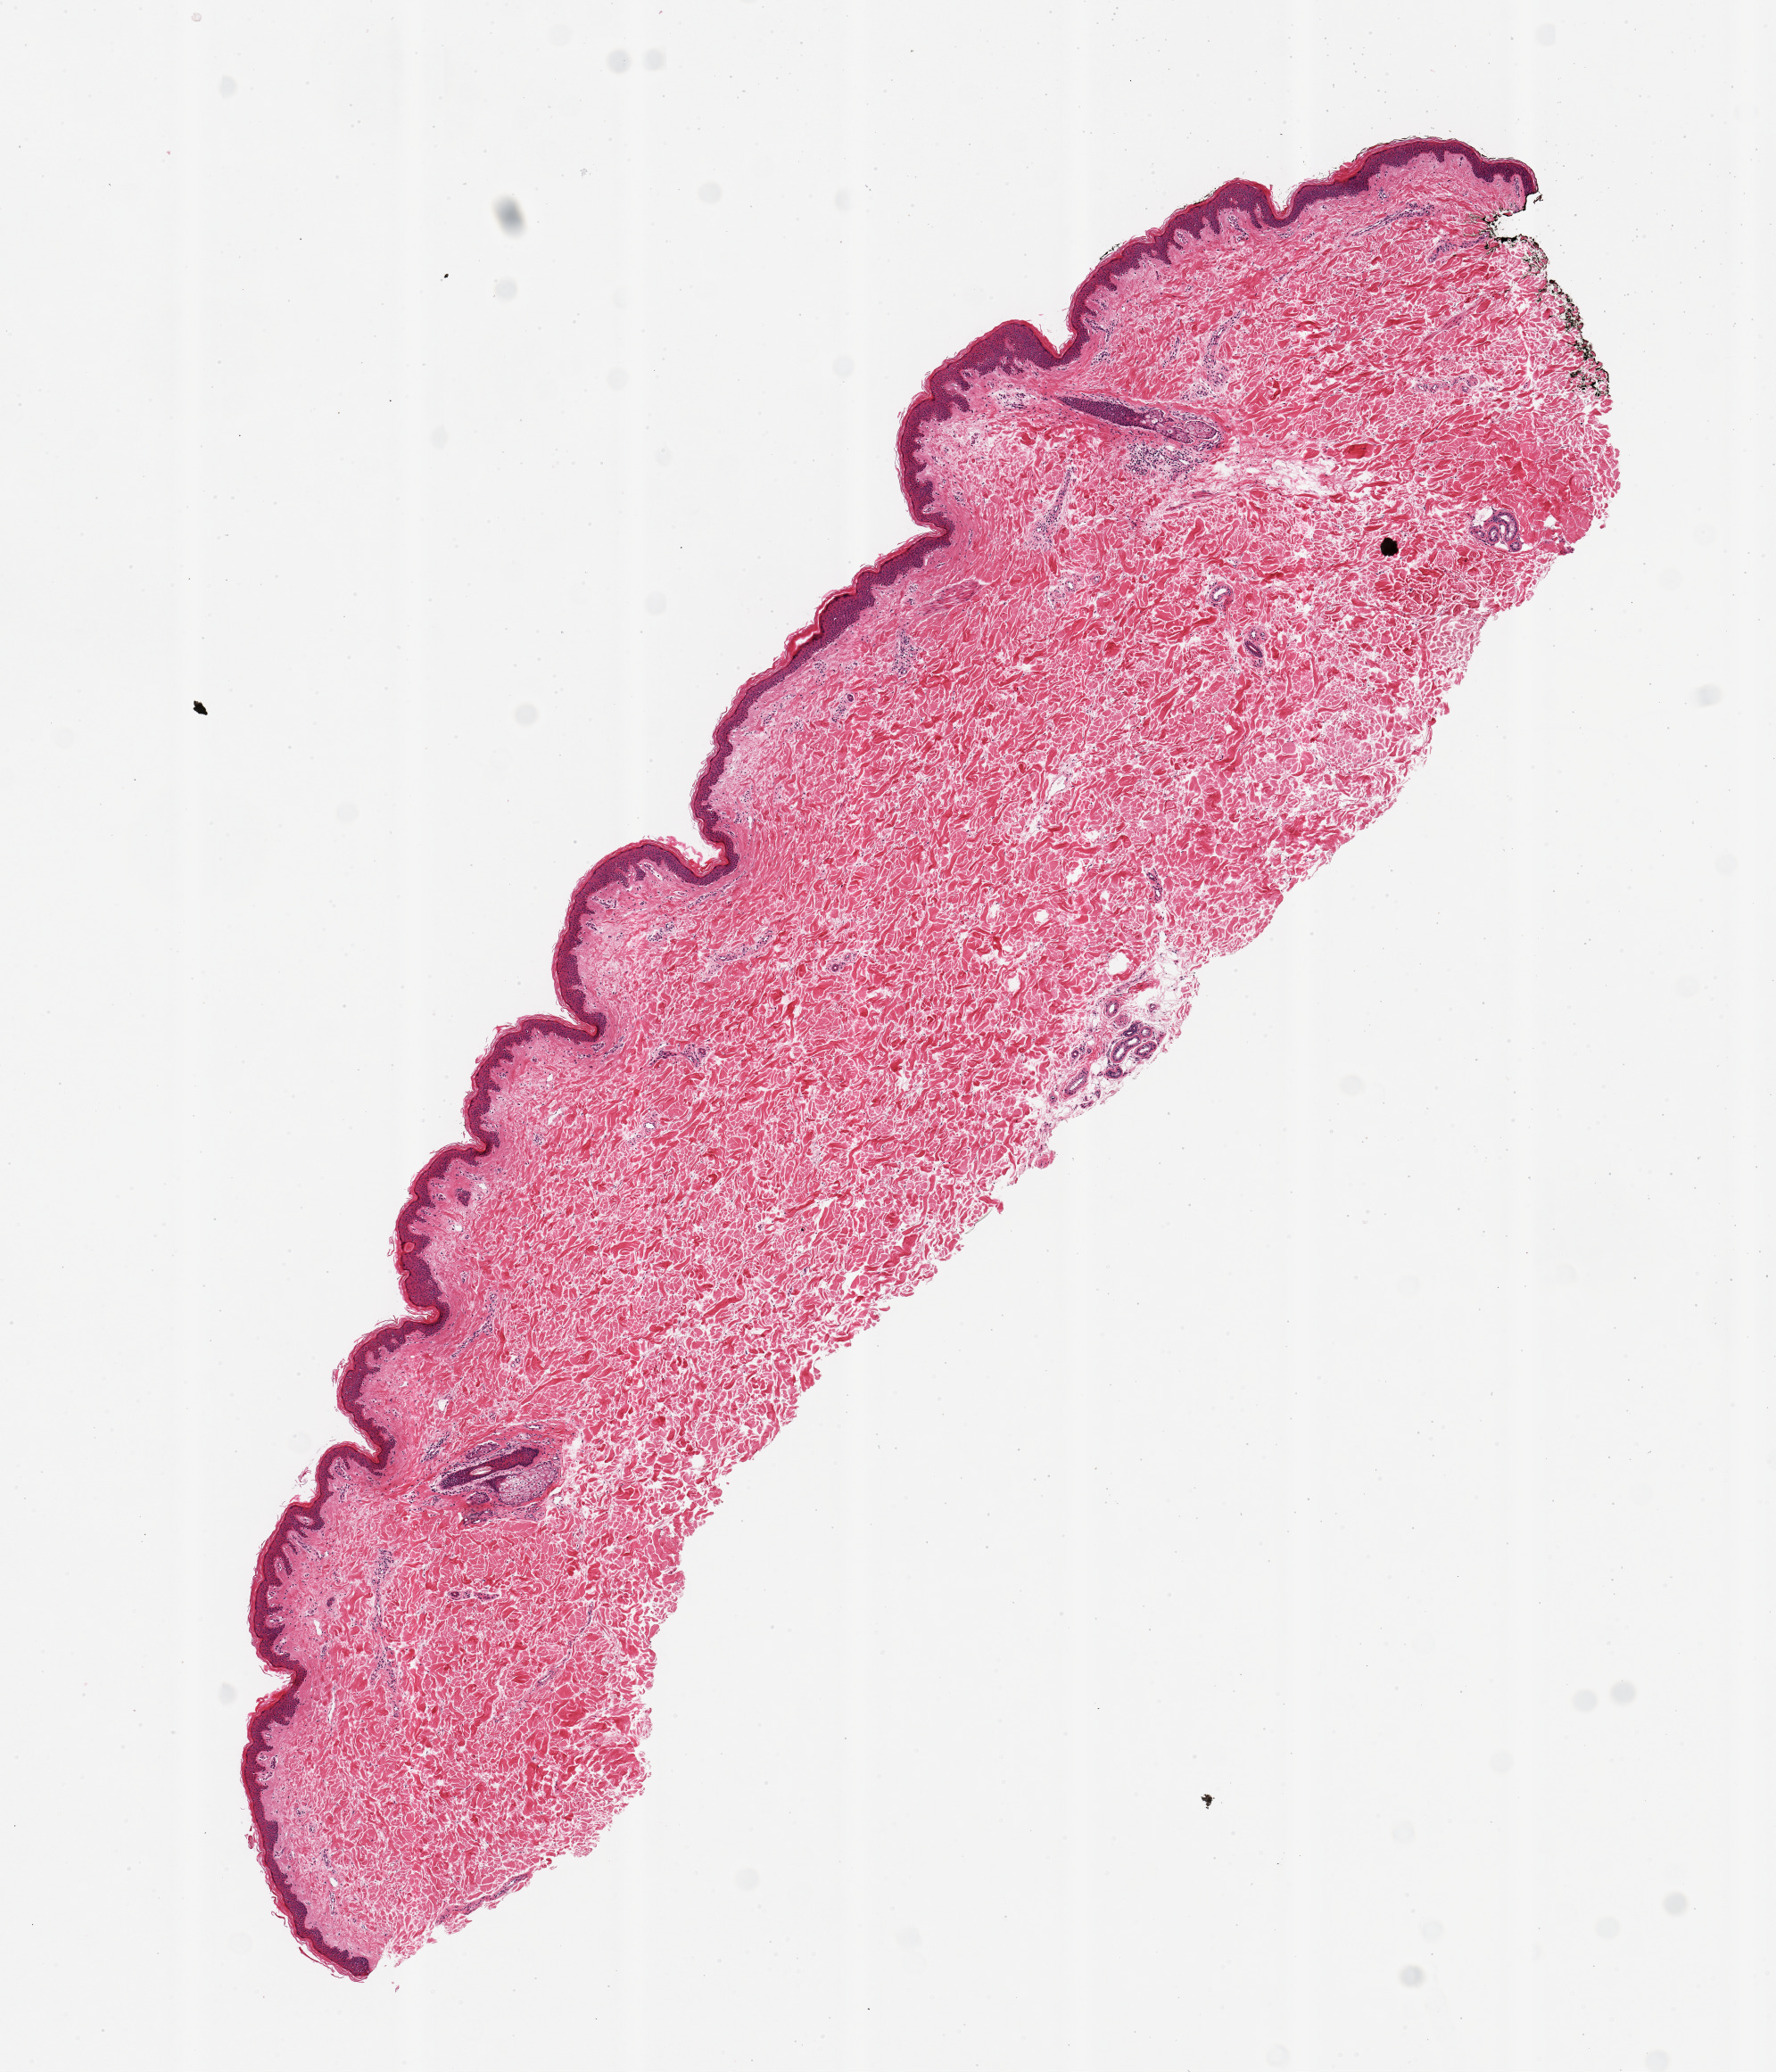
Whole-slide image, haematoxylin and eosin stain, shown as a low-resolution overview of the whole scanned area (about 7.9 x 9.2 mm), PAXgene-fixed, paraffin-embedded tissue, target tissue: skin of lower leg, tissue donor sample.
Reviewer comment on this tissue sample: 1 piece 5x3mm; well trimmed.